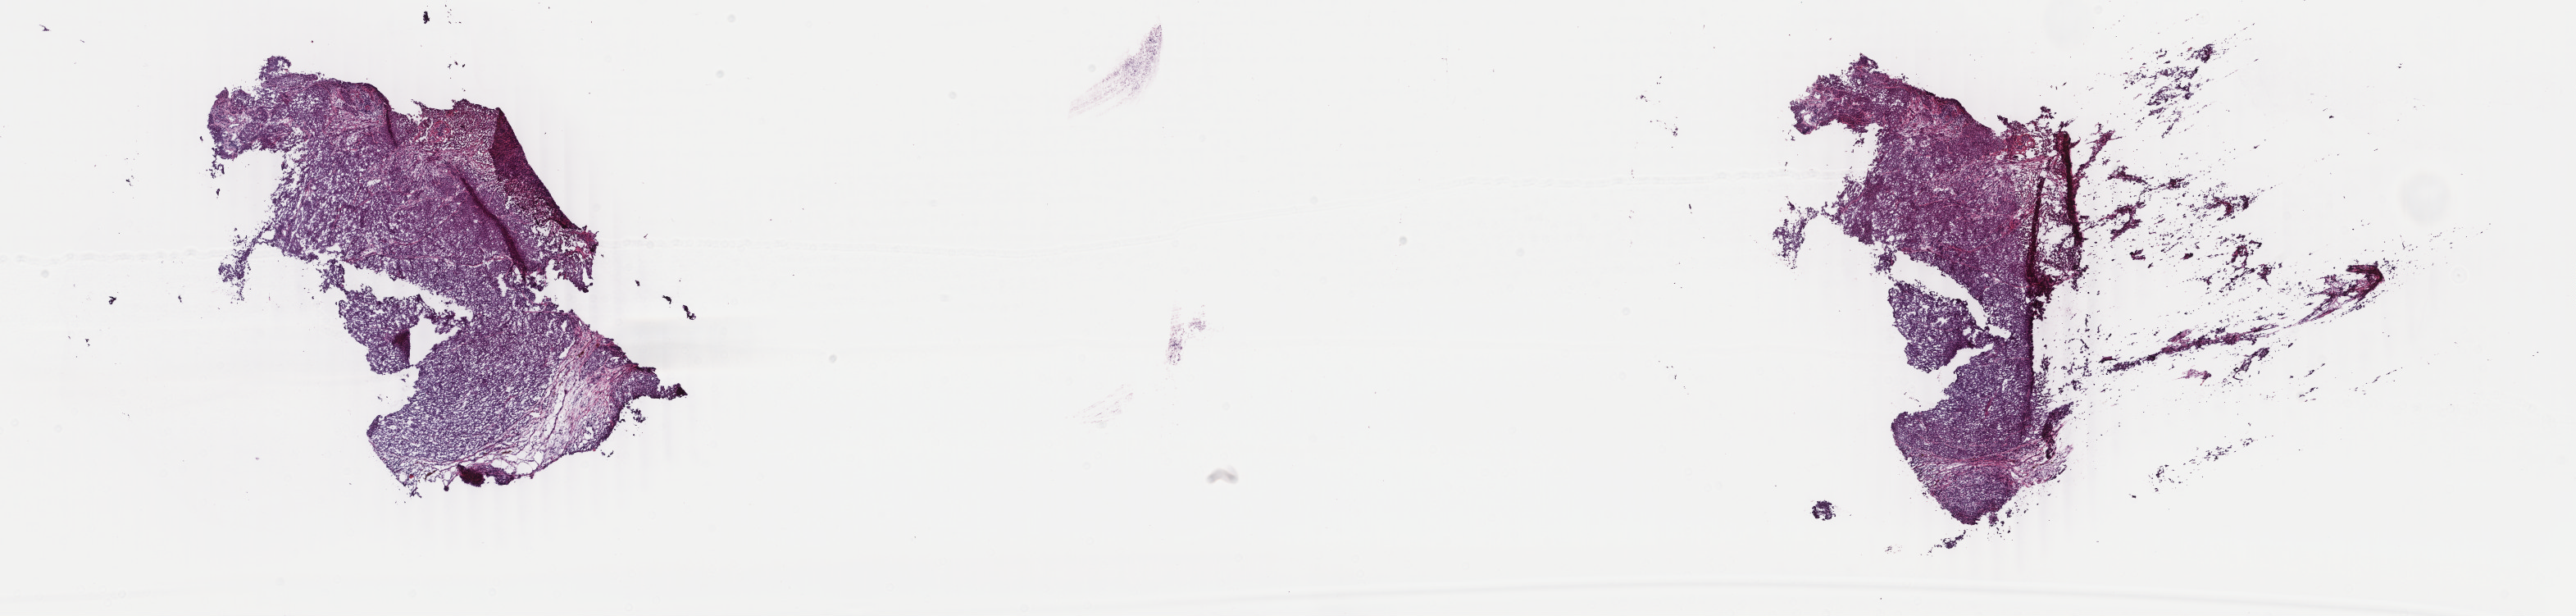
H&E-stained whole-slide image — low-resolution overview of the scanned area, about 25.0 x 6.0 mm. Frozen section. Skin, primary tumour sample. Patient: female, age at initial diagnosis 74 years. Composition of this section per pathologist review: tumour cells 95%, tumour nuclei 95%.
Diagnosis: Malignant melanoma, NOS.